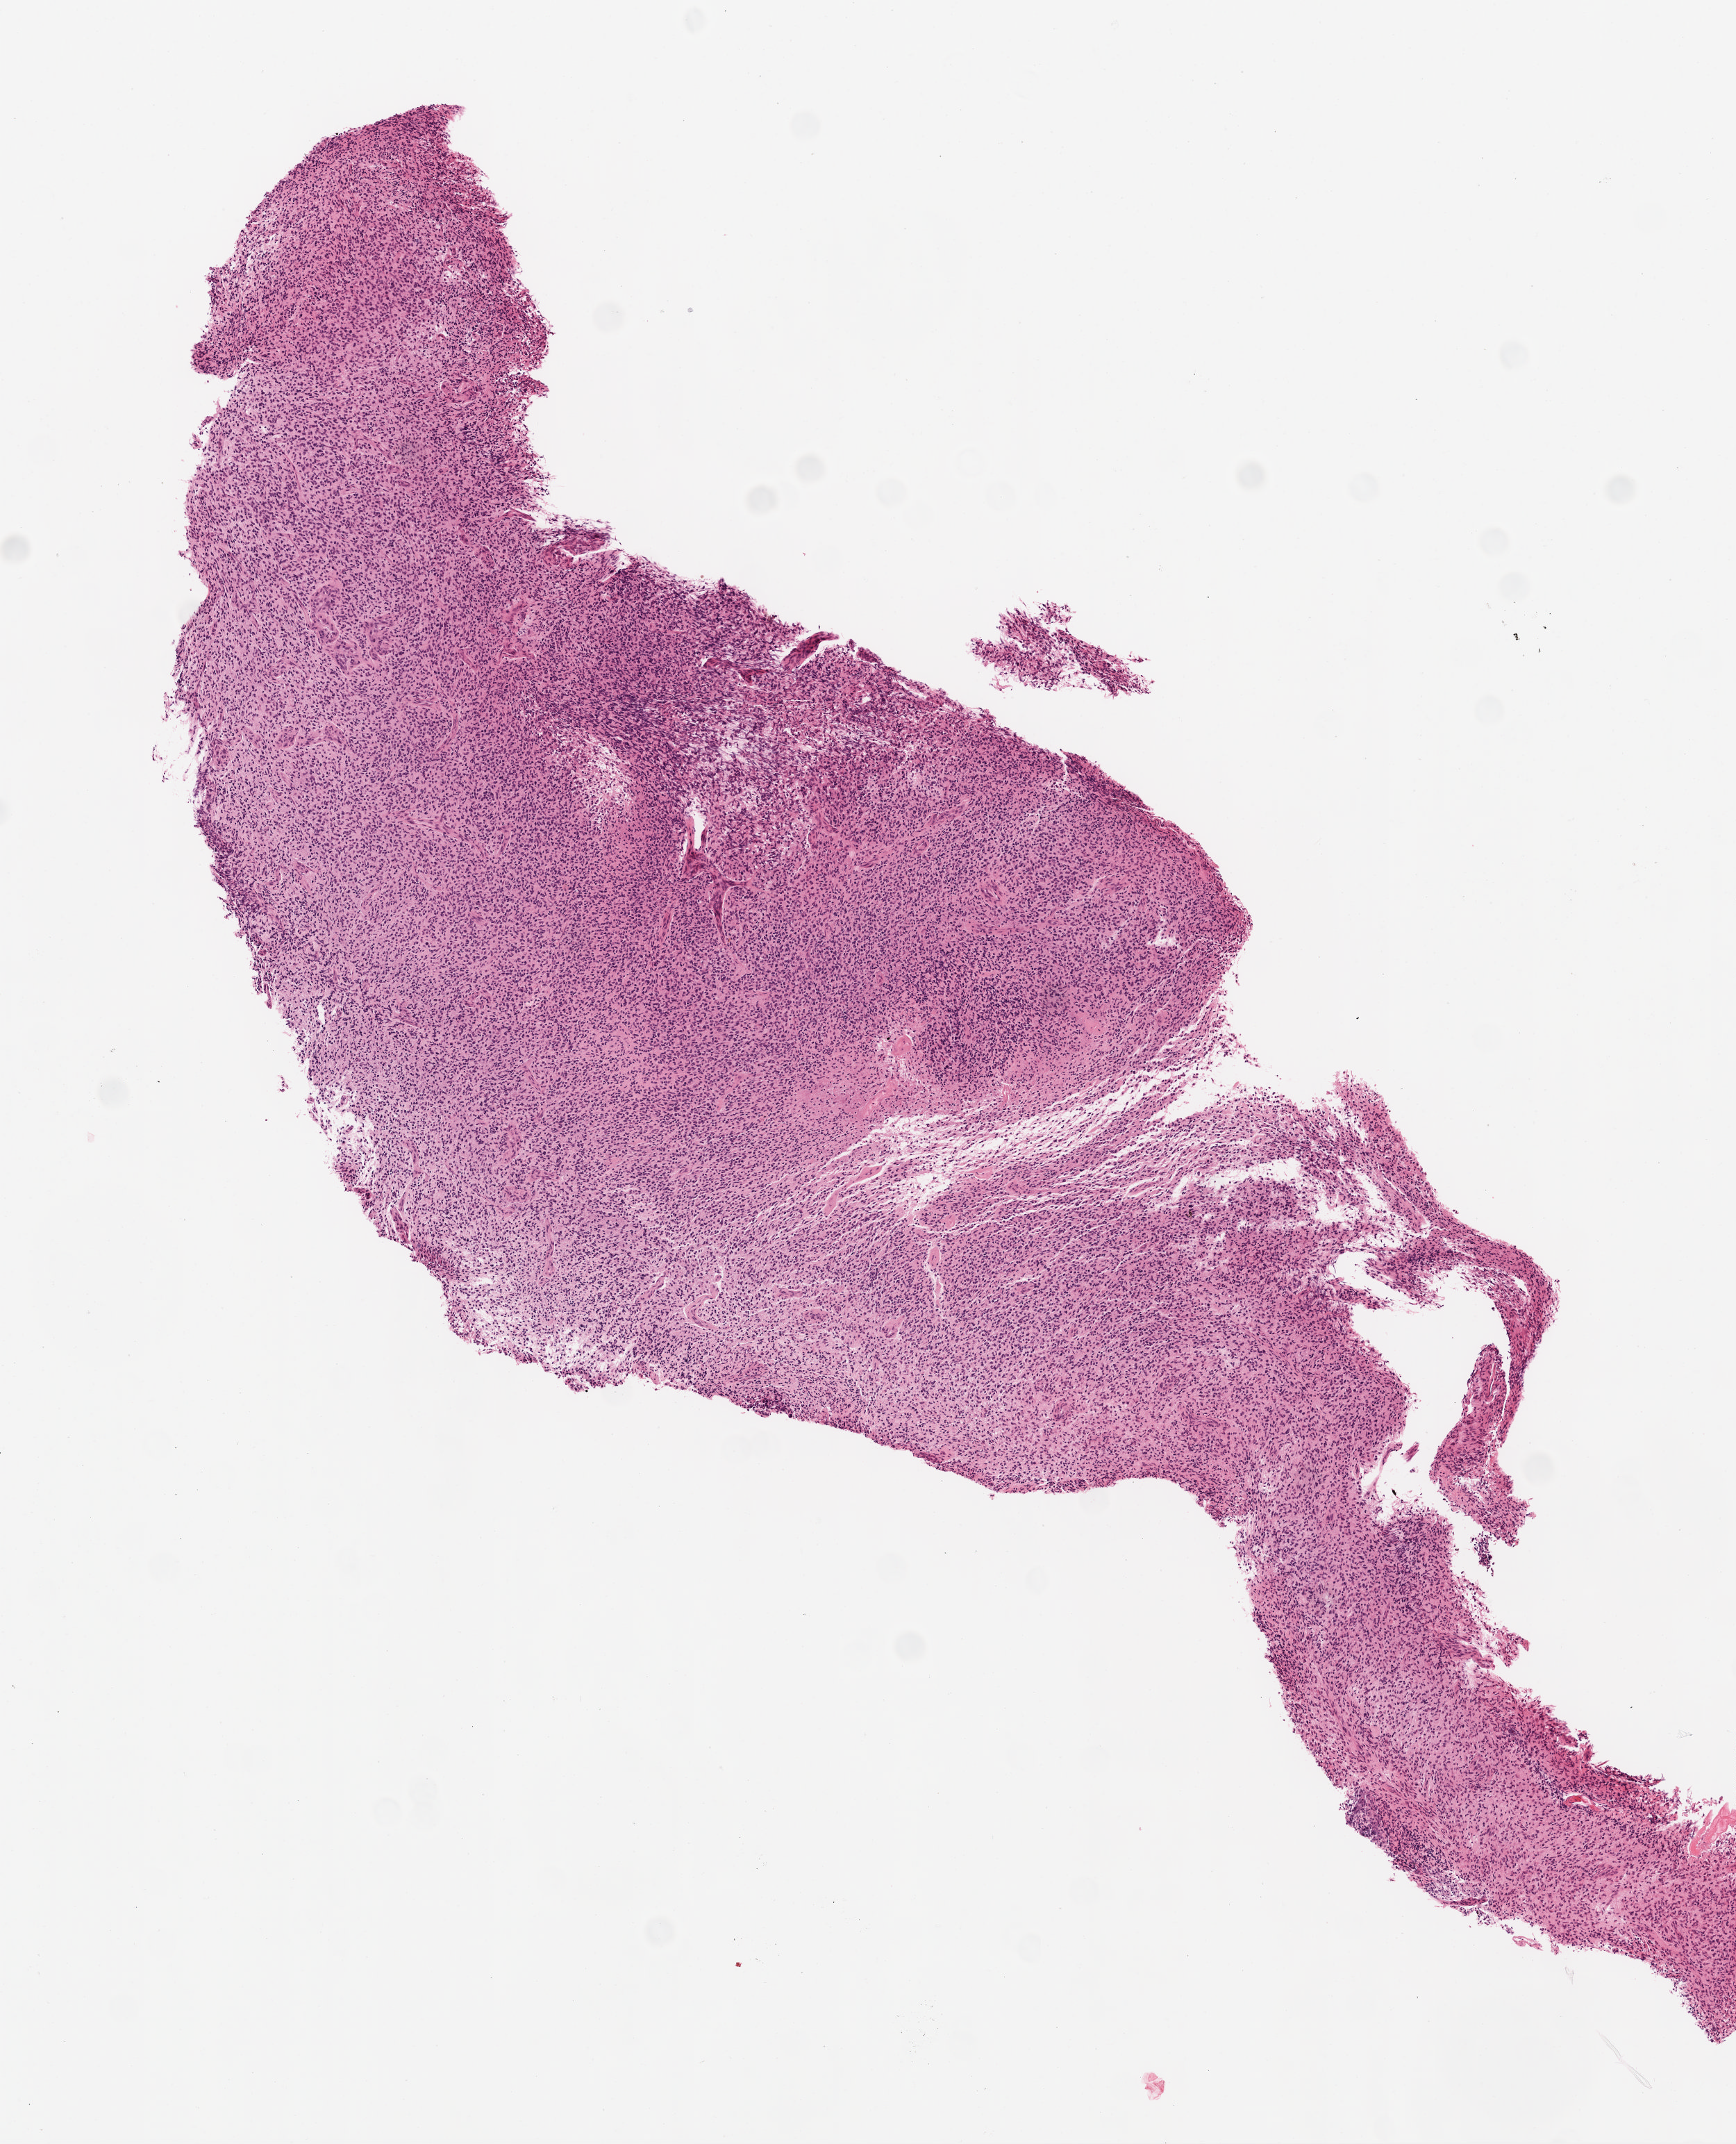
Whole-slide histology image, H&E-stained — whole scanned area (about 5.0 x 6.2 mm, acquisition: 20x scan) shown as a low-resolution overview. Formalin-fixed paraffin-embedded (FFPE) diagnostic section. Sample: primary tumour, brain. Female patient; age at initial diagnosis 56 years.
* histologic diagnosis: Glioblastoma